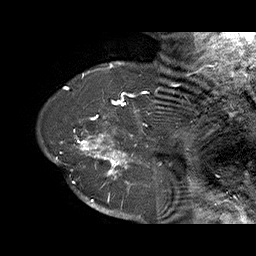
Breast MRI (dynamic contrast-enhanced), one sagittal slice; slice 57 of 70 in the series (ordered by position); dynamic contrast-enhanced series, time point 2 of 6 at this slice position (early post-contrast); 1.5 T; TE 4.5 ms, TR 32.4 ms; 3 mm slice thickness; 256 × 256 image matrix, field of view 180 × 180 mm. Female patient. From the clinical record (not read from this slice): setting: breast cancer imaged before/during neoadjuvant chemotherapy; receptor status: HR-positive, HER2-negative.
Structures marked on this image (semi-automatic segmentation, software-assisted and operator-edited):
- analysis volume of interest (the breast-tissue region the enhancement analysis was run in; not a lesion): bounding box [x1, y1, x2, y2] px = [71, 128, 159, 202]
- tumour enhancement mask (voxels above the 100 % enhancement threshold inside the analysis volume of interest): [71, 129, 150, 202]